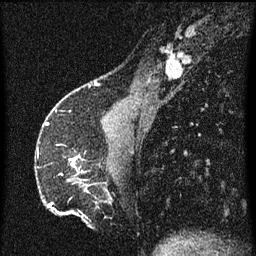
Breast MRI (dynamic contrast-enhanced), one sagittal slice. Position 19 of 60 along the scan axis. Dynamic contrast-enhanced series, image 2 of 3 at this slice position (ordered by acquisition). 1.5 T. TE 4.2 ms, TR 8 ms. 2 mm slice thickness. 256 × 256 image matrix. Patient: female, 51 years.
Structures marked on this image (semi-automatic segmentation, software-assisted and operator-edited):
- analysis volume of interest (the breast-tissue region the enhancement analysis was run in; not a lesion): bounding box (x1, y1, x2, y2) in pixels: (70, 156, 87, 173)
- tumour enhancement mask (voxels above the 70 % enhancement threshold inside the analysis volume of interest): (70, 156, 81, 169)